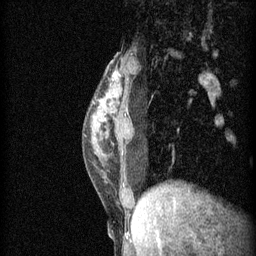
Breast MRI (dynamic contrast-enhanced), one sagittal slice. Slice 19 of 60 in the series (ordered by position). 3 images stored at this slice position (order not interpretable as contrast timing). 1.5 T. TE 4.2 ms, TR 11 ms. 2 mm slice thickness. 256 × 256 image matrix, field of view 180 × 180 mm. Patient: female, 40 years.
Annotated regions visible in this slice (semi-automatic segmentation, software-assisted and operator-edited):
- analysis volume of interest (the breast-tissue region the enhancement analysis was run in; not a lesion): bounding box (x1, y1, x2, y2) in pixels: (84, 54, 165, 191)
- tumour enhancement mask (voxels above the 70 % enhancement threshold inside the analysis volume of interest): (114, 74, 117, 79)